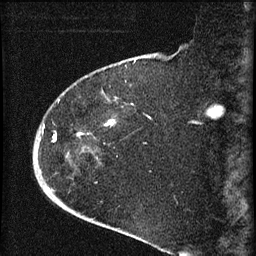
Breast MRI (dynamic contrast-enhanced), one sagittal slice; slice 17 of 60 in the series (ordered by position); dynamic contrast-enhanced series, image 2 of 4 at this slice position (ordered by acquisition); 1.5 T; TE 4.2 ms, TR 8.2 ms; 2 mm slice thickness; 256 × 256 image matrix, field of view 180 × 180 mm. Patient: female, 71 years.
Structures marked on this image (semi-automatically segmented with operator editing):
- analysis volume of interest (the breast-tissue region the enhancement analysis was run in; not a lesion): bounding box <35,76,125,190> (left, top, right, bottom; pixels)
- tumour enhancement mask (voxels above the 70 % enhancement threshold inside the analysis volume of interest): <54,121,113,142>